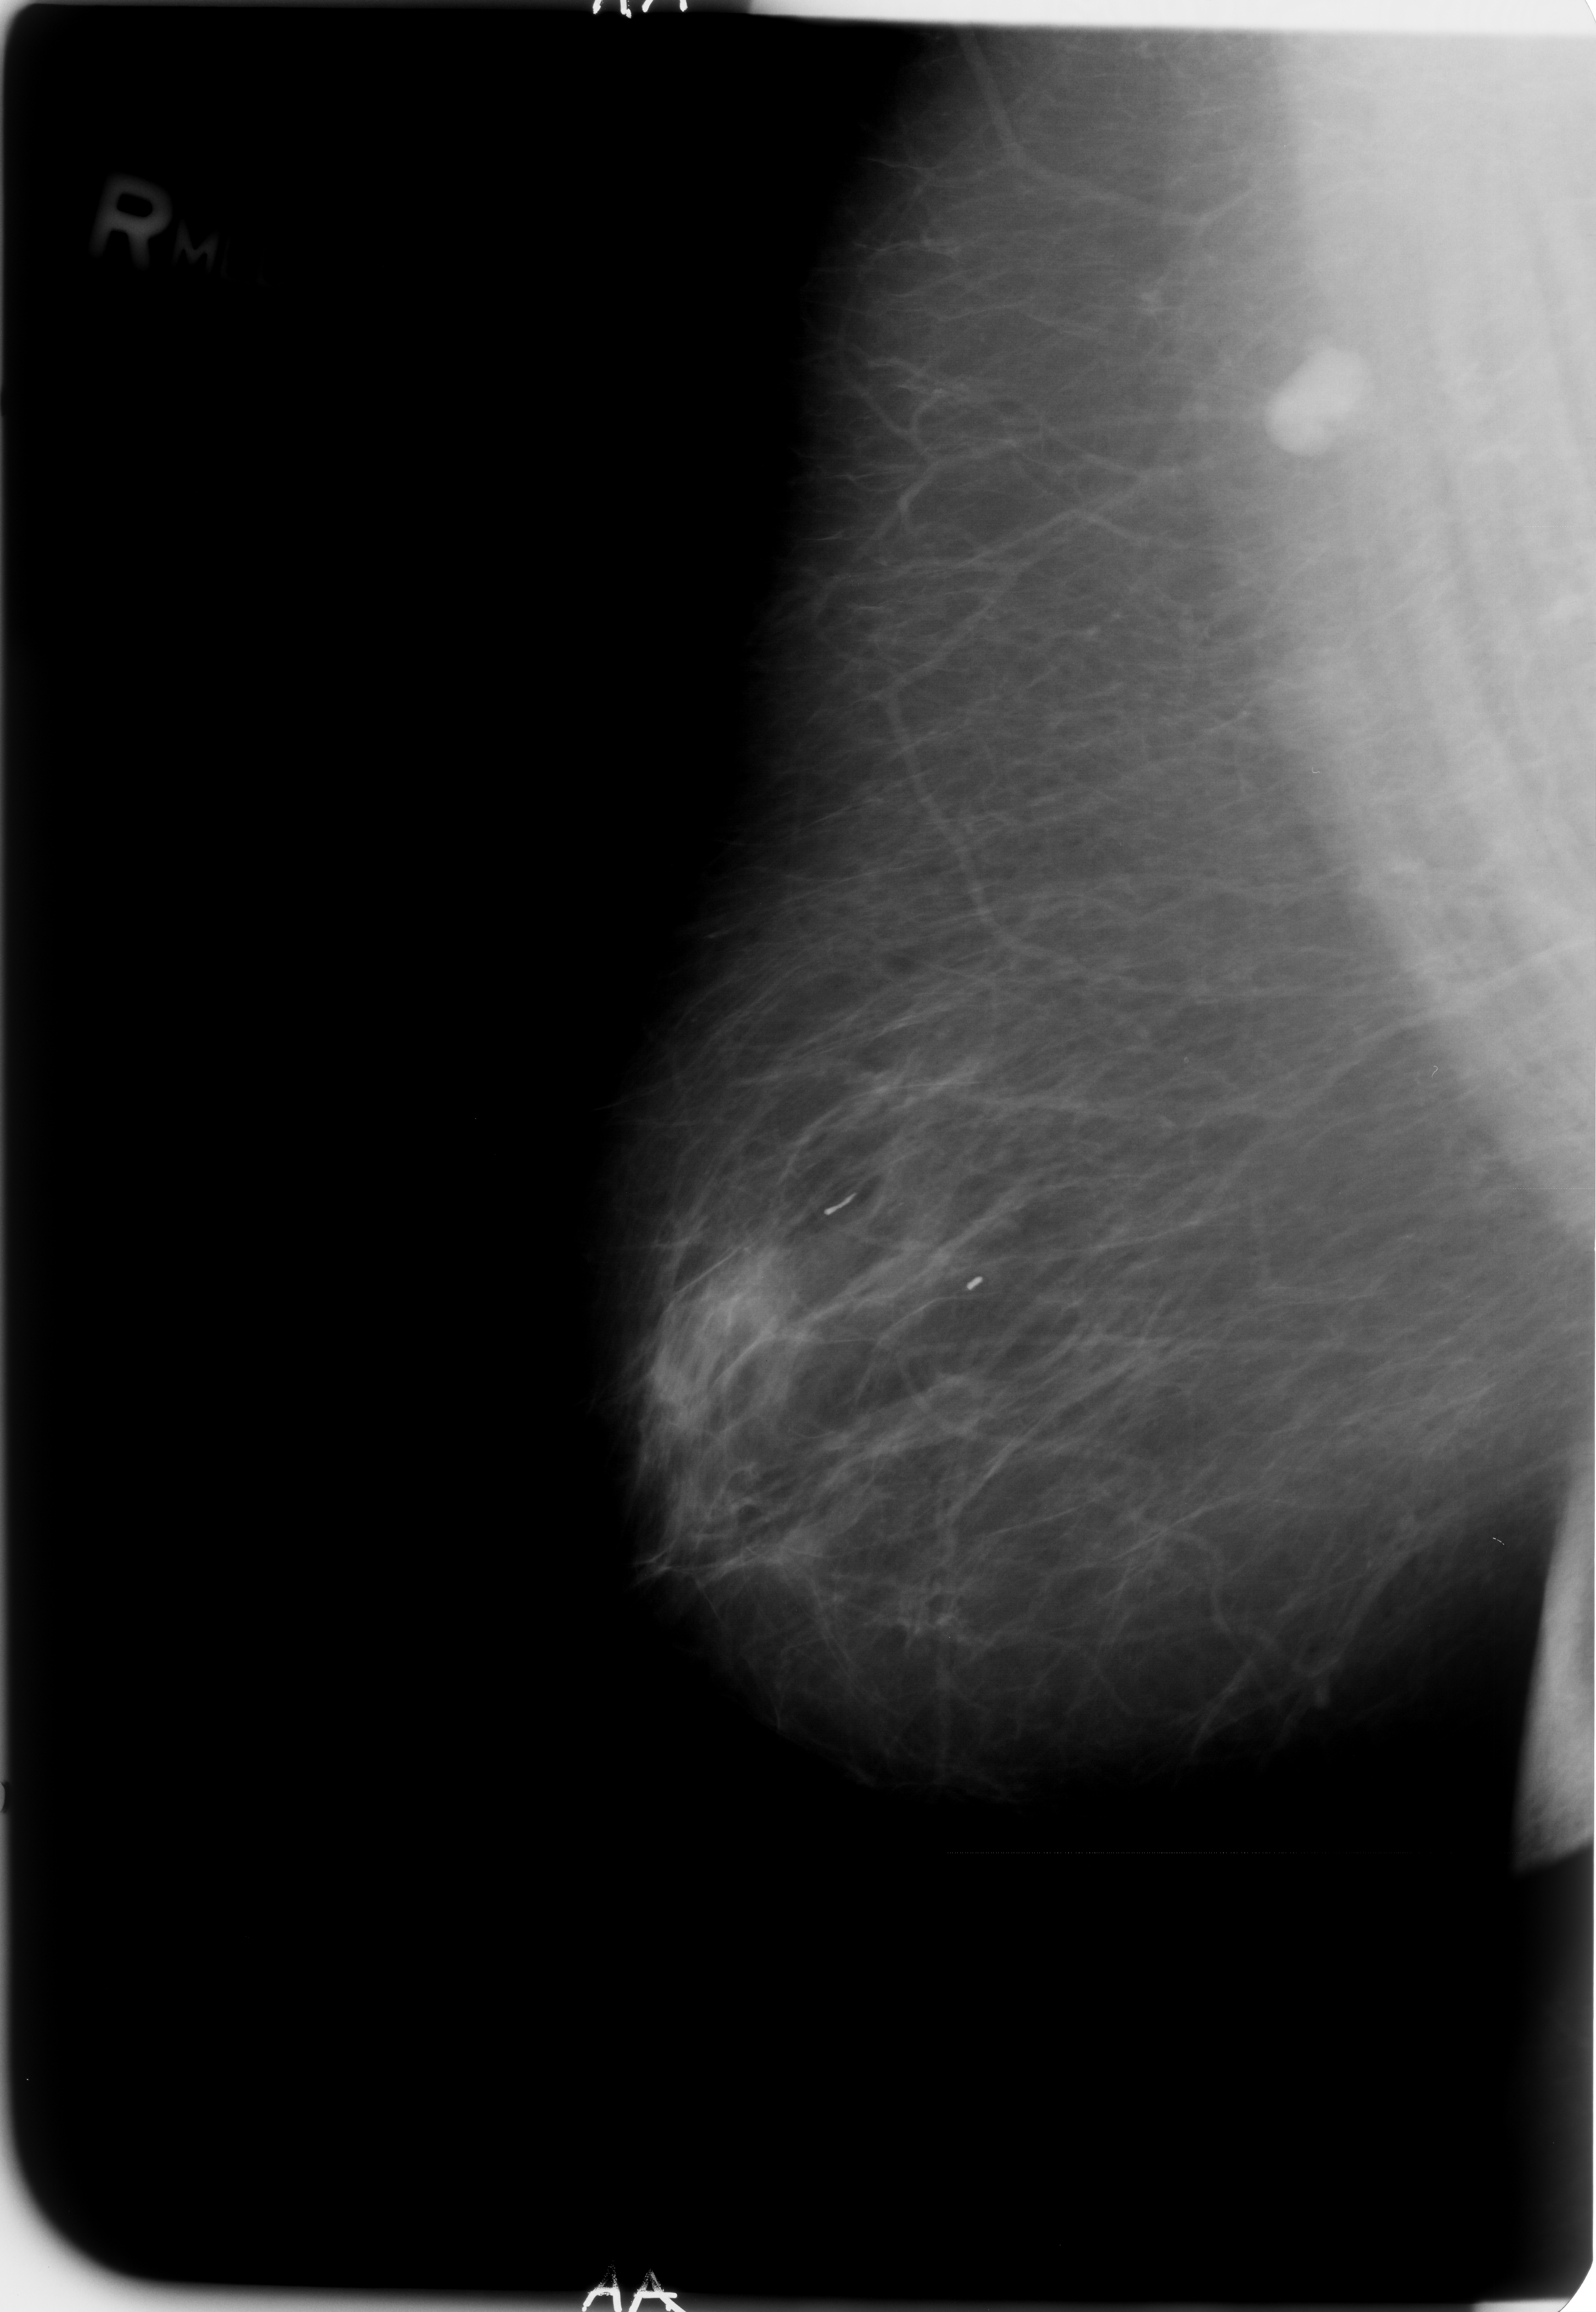
Scanned film-screen mammogram, right breast, MLO view, breast composition: almost entirely fatty (BI-RADS density category 1 of 4).
- Abnormality record for this image: Finding 1 of 2: calcifications, morphology large rodlike, distribution segmental; BI-RADS assessment category 2; benign; no additional work-up was recommended (benign without callback).
- Finding 2 of 2: calcifications, morphology large rodlike, distribution segmental; BI-RADS assessment category 2; subtlety rating 5 on a 1 (subtle) to 5 (obvious) scale; benign without callback (not worked up further).